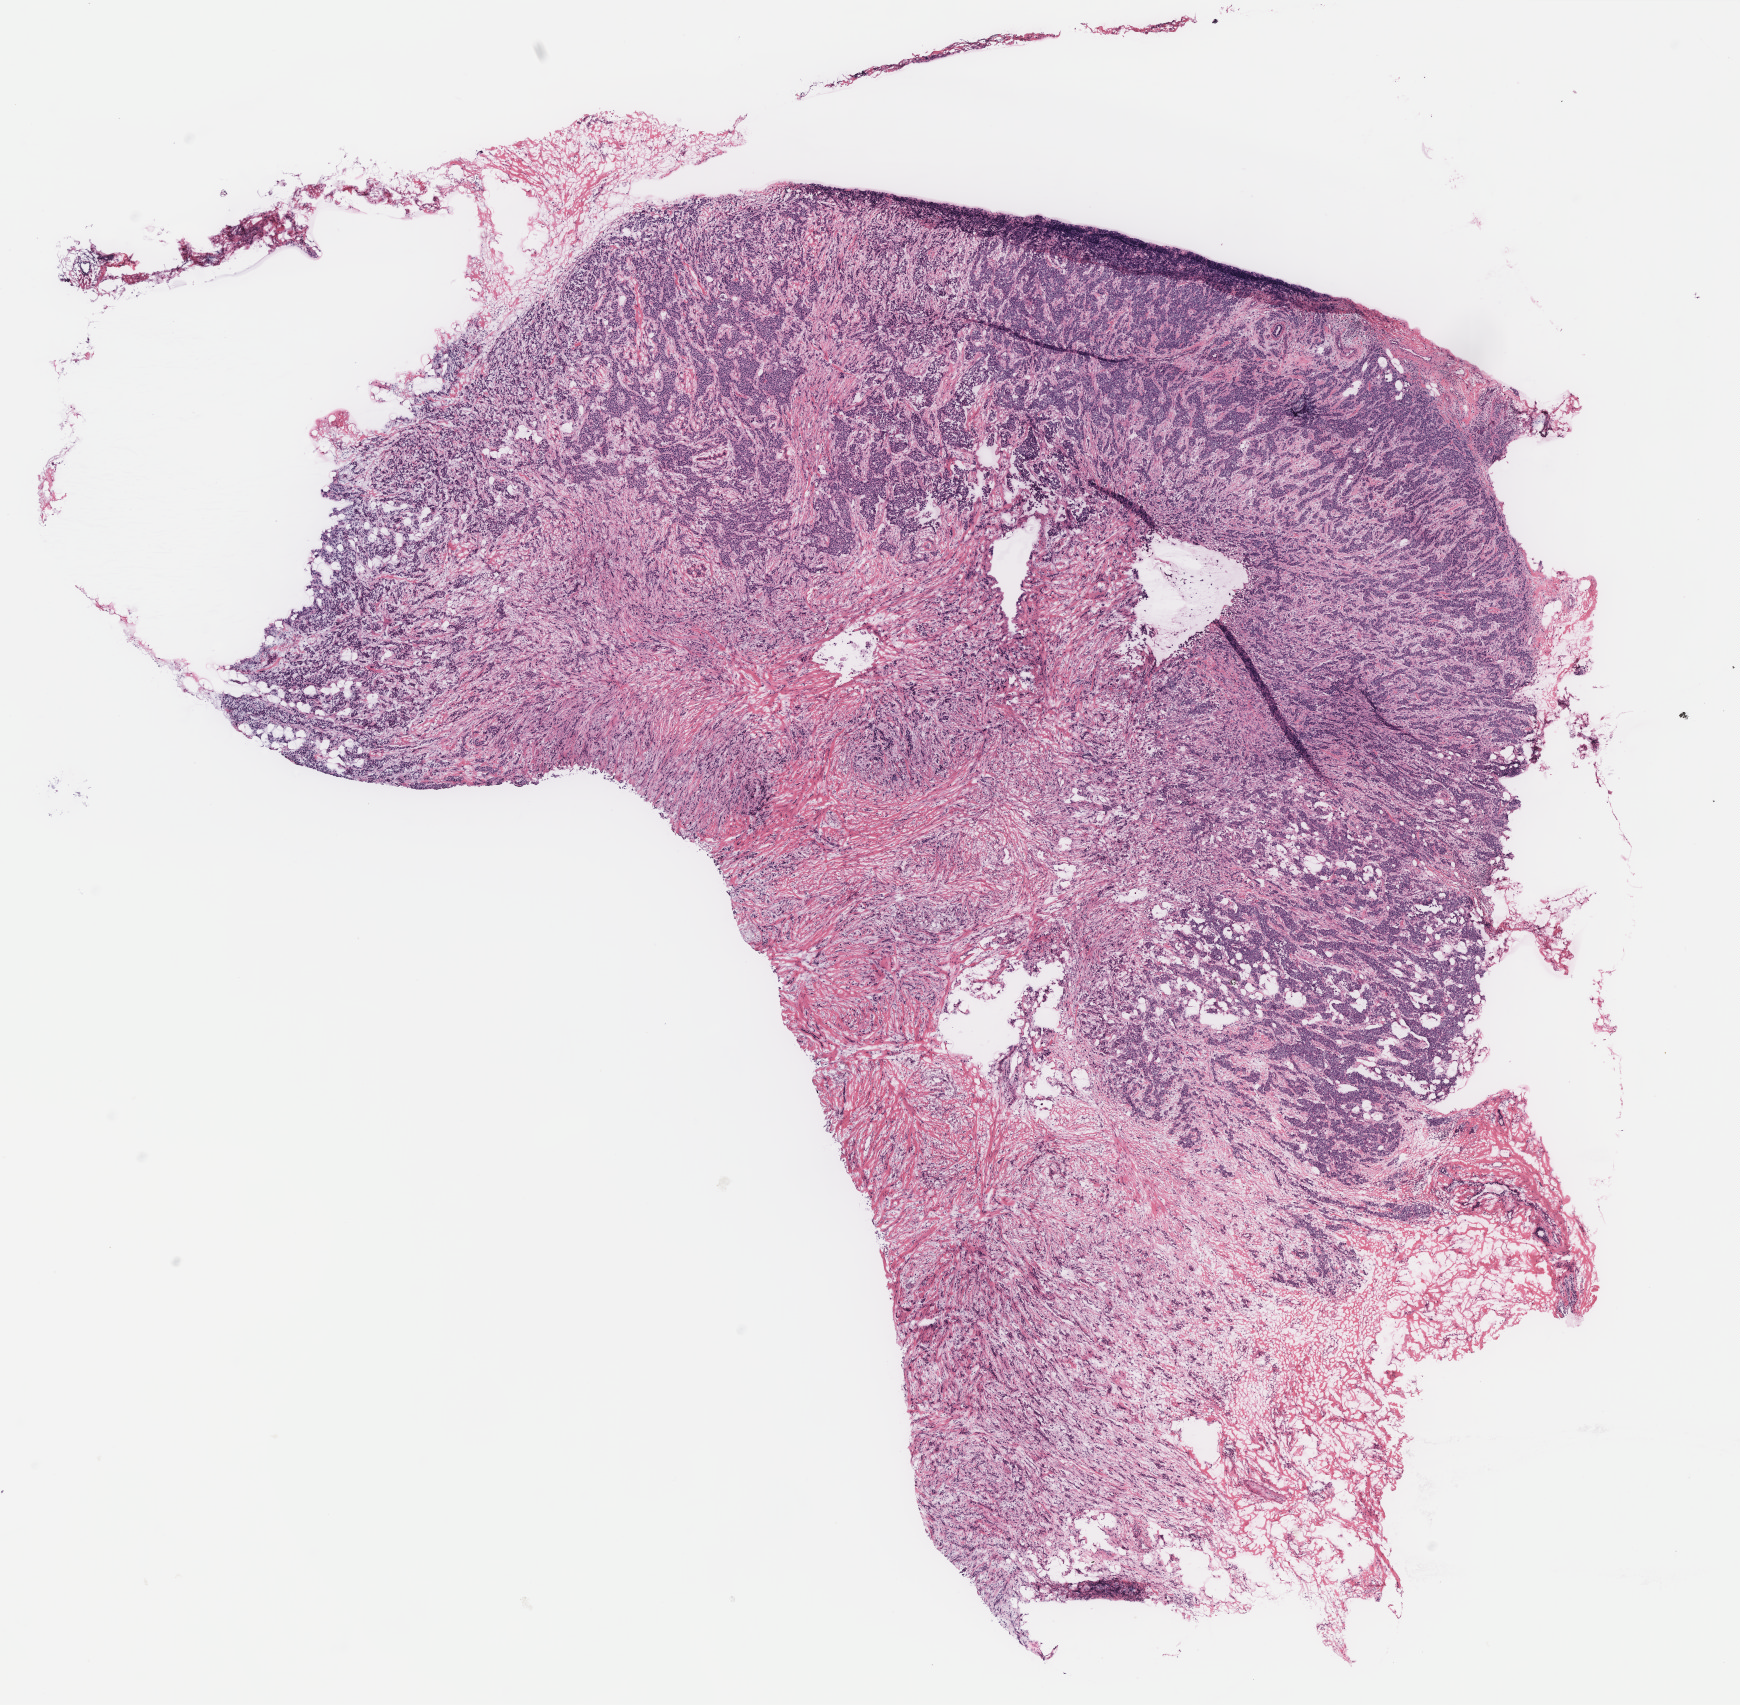
Digitized Hematoxylin and eosin (H&E) stained tissue section (whole slide), a low-resolution overview of the entire scanned area, about 13.9 x 13.6 mm (from a 40x scan), breast, tissue type not recorded.
Patient diagnosis (cohort enrolment): breast cancer (breast).